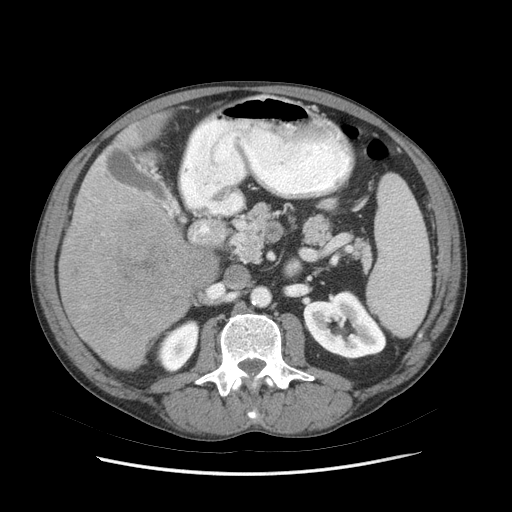
Contrast-enhanced abdominal CT (liver protocol), one axial slice. Slice 30 of 89 in the series (ordered by position). Reconstruction kernel STANDARD. 140 kVp. Soft-tissue window (W 400 / L 40 HU). 2.5 mm slice thickness. 512 × 512 image matrix, field of view 380 × 380 mm. From the clinical record (not read from this slice): diagnosis: hepatocellular carcinoma (patient treated with transarterial chemoembolisation; whether this scan precedes or follows treatment is not stated here); TNM stage (as recorded): Stage-IIIB; Child-Pugh class: A; tumour differentiation: moderately differentiated; tumour nodularity: multinodular.
Structures marked on this image (semi-automatically segmented with operator editing):
- liver parenchyma outside the tumour (the mass and vessels are separate outlines, so this box may not span the whole liver): bounding box [x1, y1, x2, y2] px = [58, 112, 217, 370]
- mass: [60, 206, 215, 368]
- liver vessels: [164, 206, 172, 215]